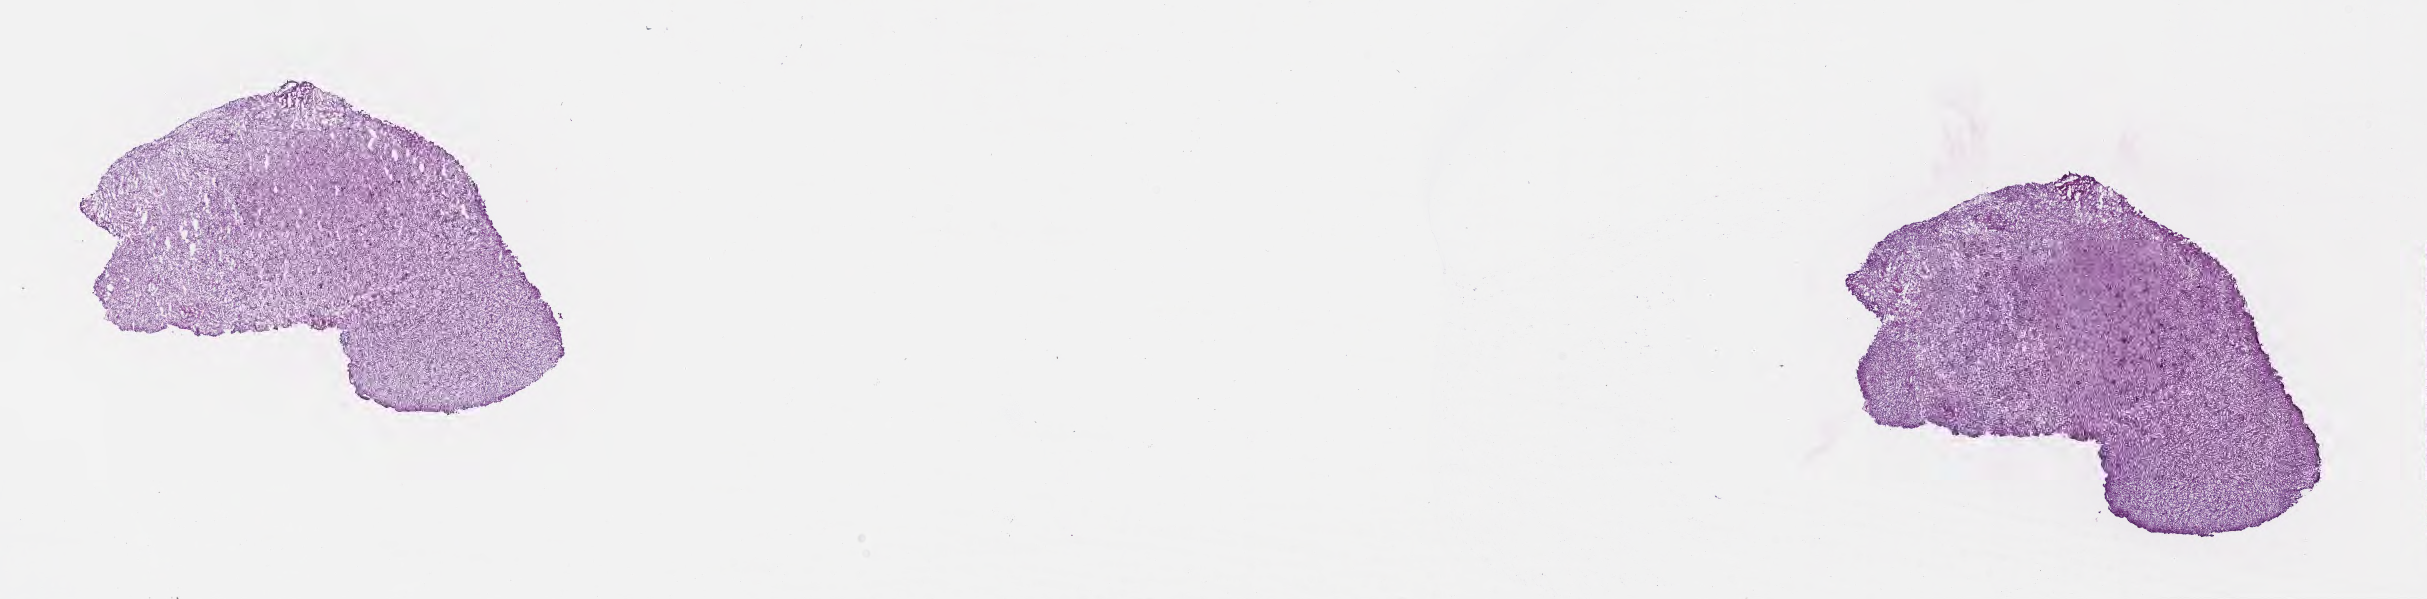
H&E whole-slide image — whole scanned area (about 19.6 x 4.8 mm) shown as a low-resolution overview. Frozen section (tissue freezing medium). Specimen: primary tumor. Anatomic site: brain. Patient: male, age at initial diagnosis 49 years. Pathologist review of this section (percent, as recorded): tumor cells 87%, tumor nuclei 90%, stromal cells 4%, necrosis 0%, normal cells 9%. Inflammatory infiltration, as recorded: lymphocyte infiltration 0%, monocyte infiltration 0%, neutrophil infiltration 0%.
Histologic diagnosis: Glioblastoma, NOS.